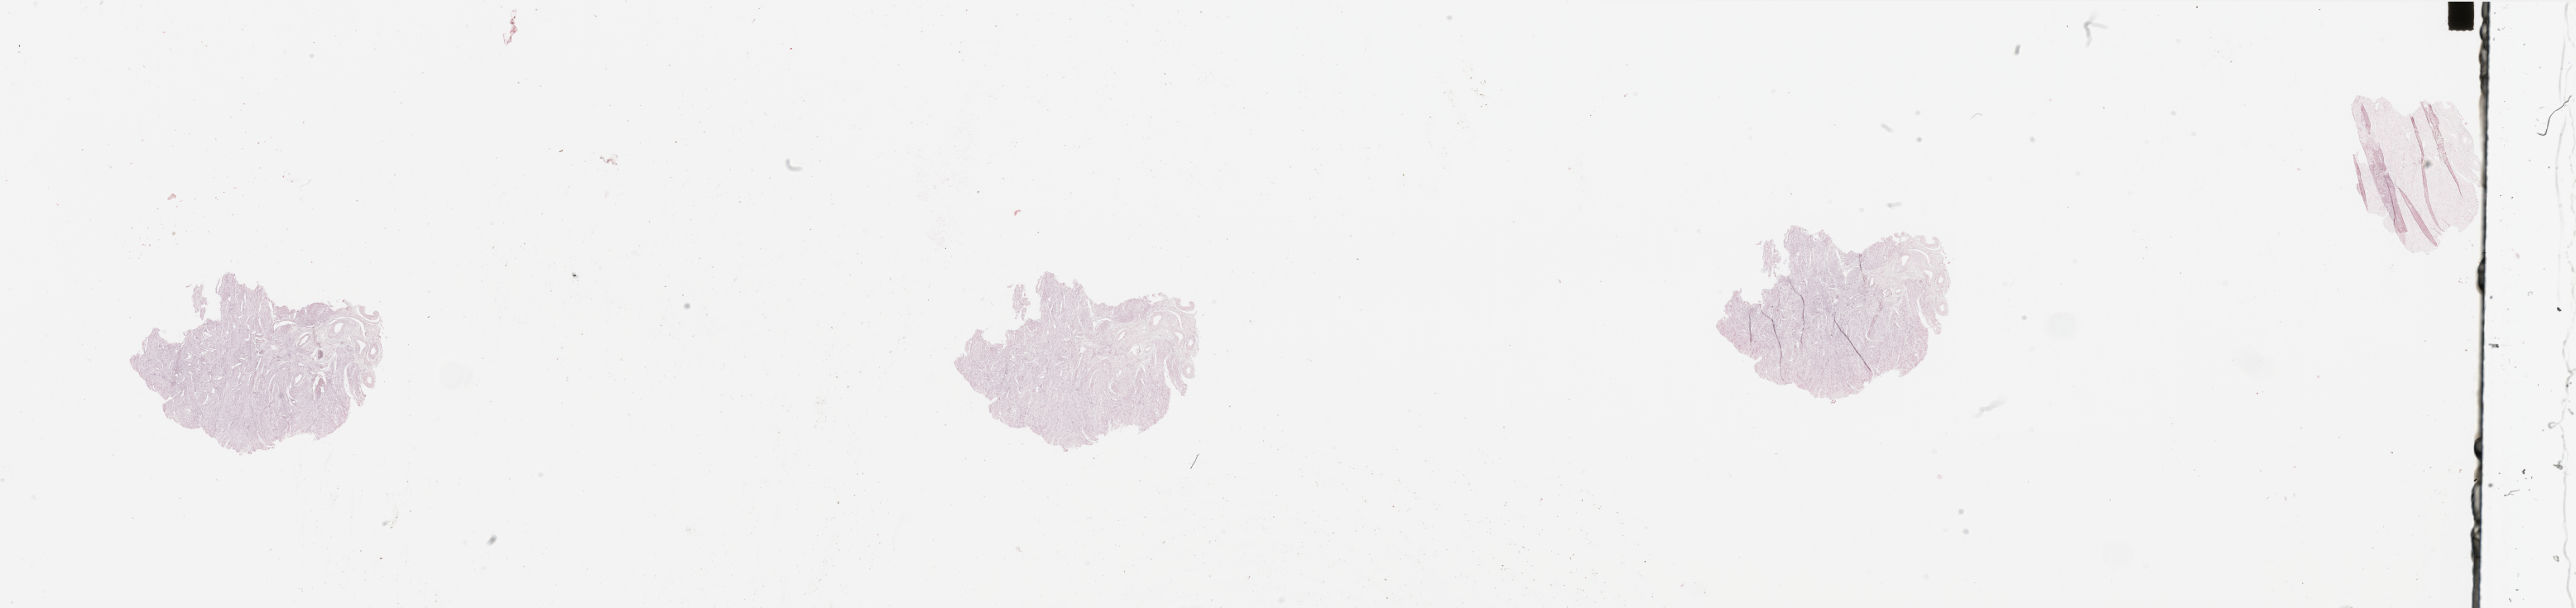
Digitized H&E-stained tissue section (whole slide), whole scanned area (about 49.2 x 11.6 mm) shown as a low-resolution overview; normal (non-tumour) tissue sample, uterus. 67-year-old female patient.
This section: normal (non-tumour) tissue from the same patient. Patient diagnosis: Endometrioid adenocarcinoma, NOS.